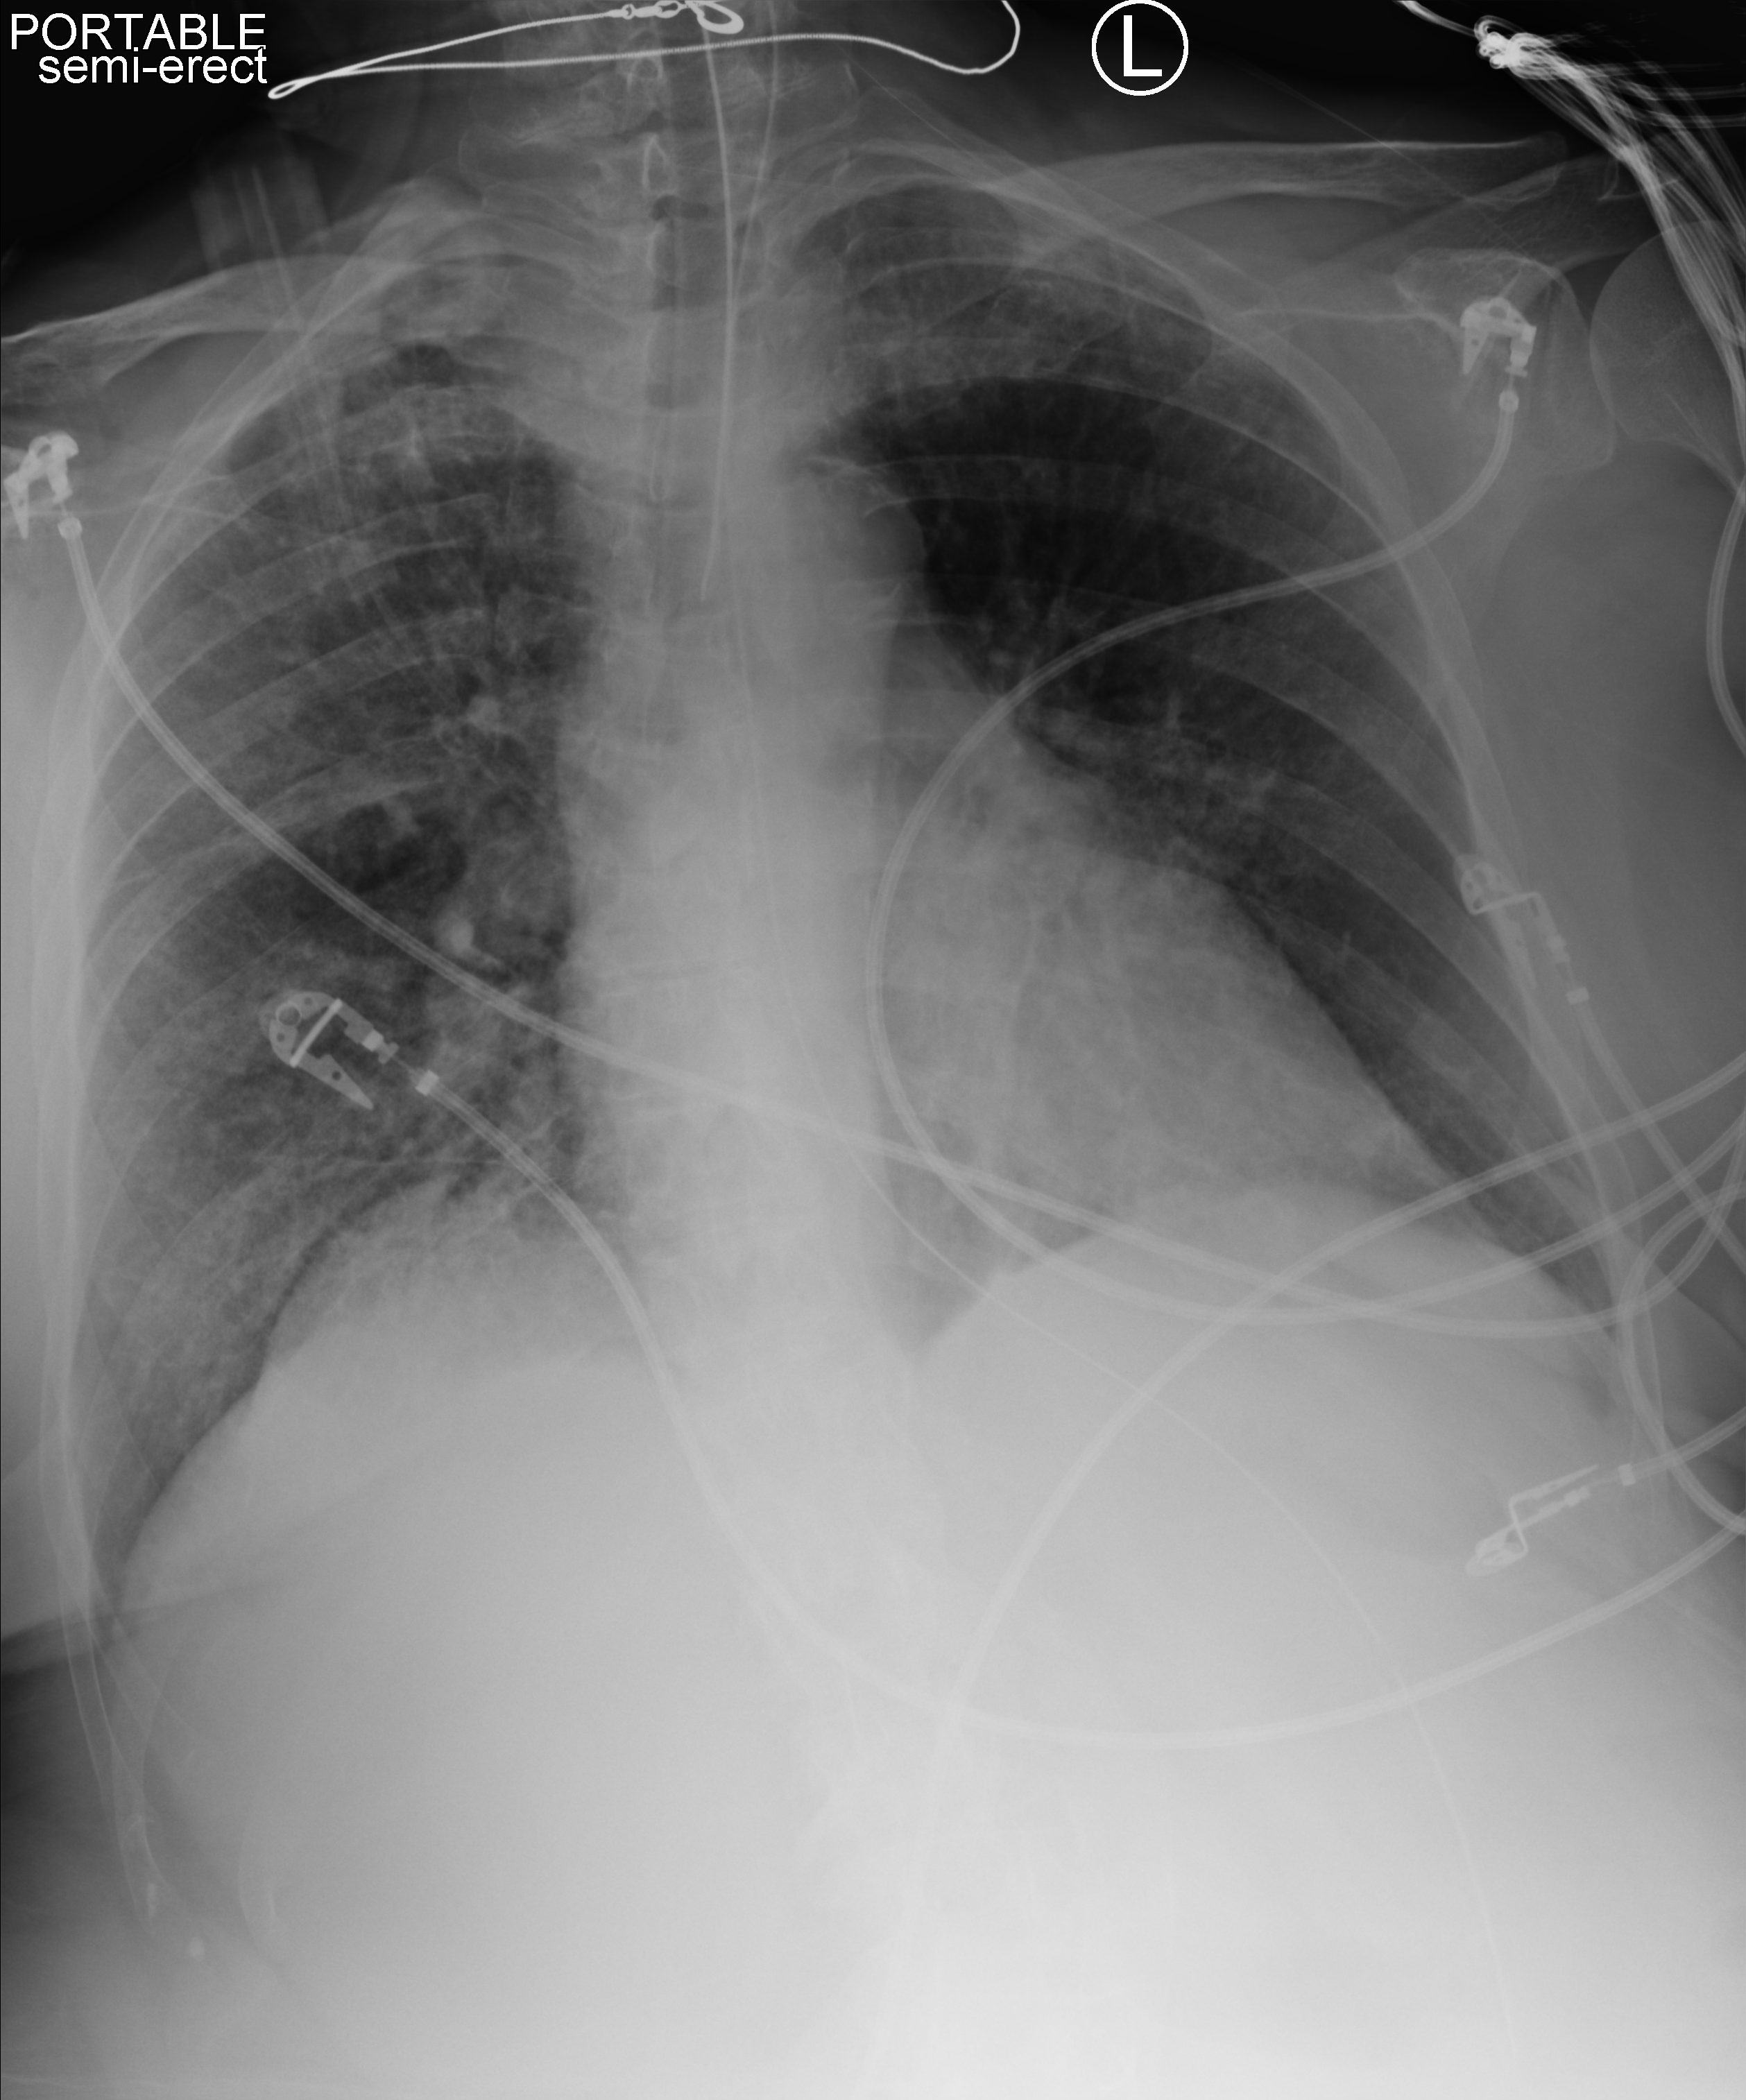
Portable chest radiograph, anteroposterior (AP) projection. Female patient hospitalised with COVID-19, age 75–90 years.
Admission-level facts for this patient (not findings on this image; timing relative to this image not recorded): other chronic lung disease (admission record): no; admitted to intensive care during this hospital stay: yes.